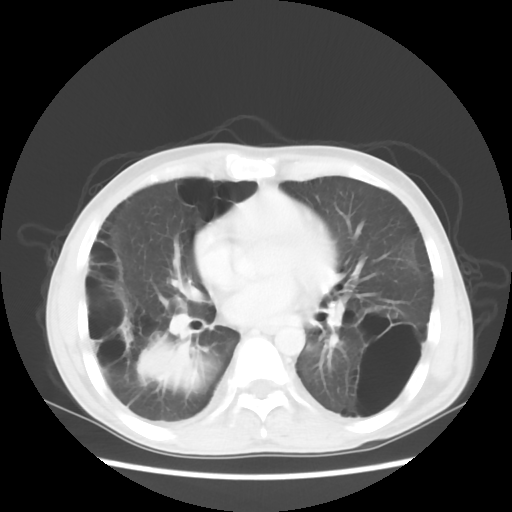
Chest CT, one axial slice; slice 25 of 56 in the series (ordered by position); 140 kVp; lung window (W 1500 / L -600 HU); 5 mm slice thickness; 512 × 512 image matrix. Male patient, age 41 years. From the clinical record (not read from this slice): clinical TNM (as recorded): T4 N0 M1a.
Annotated regions visible in this slice (rectangle marked by the reading radiologist):
- lung tumour (recorded histology: large cell carcinoma): bounding box (x1, y1, x2, y2) in pixels: (138, 339, 209, 400)